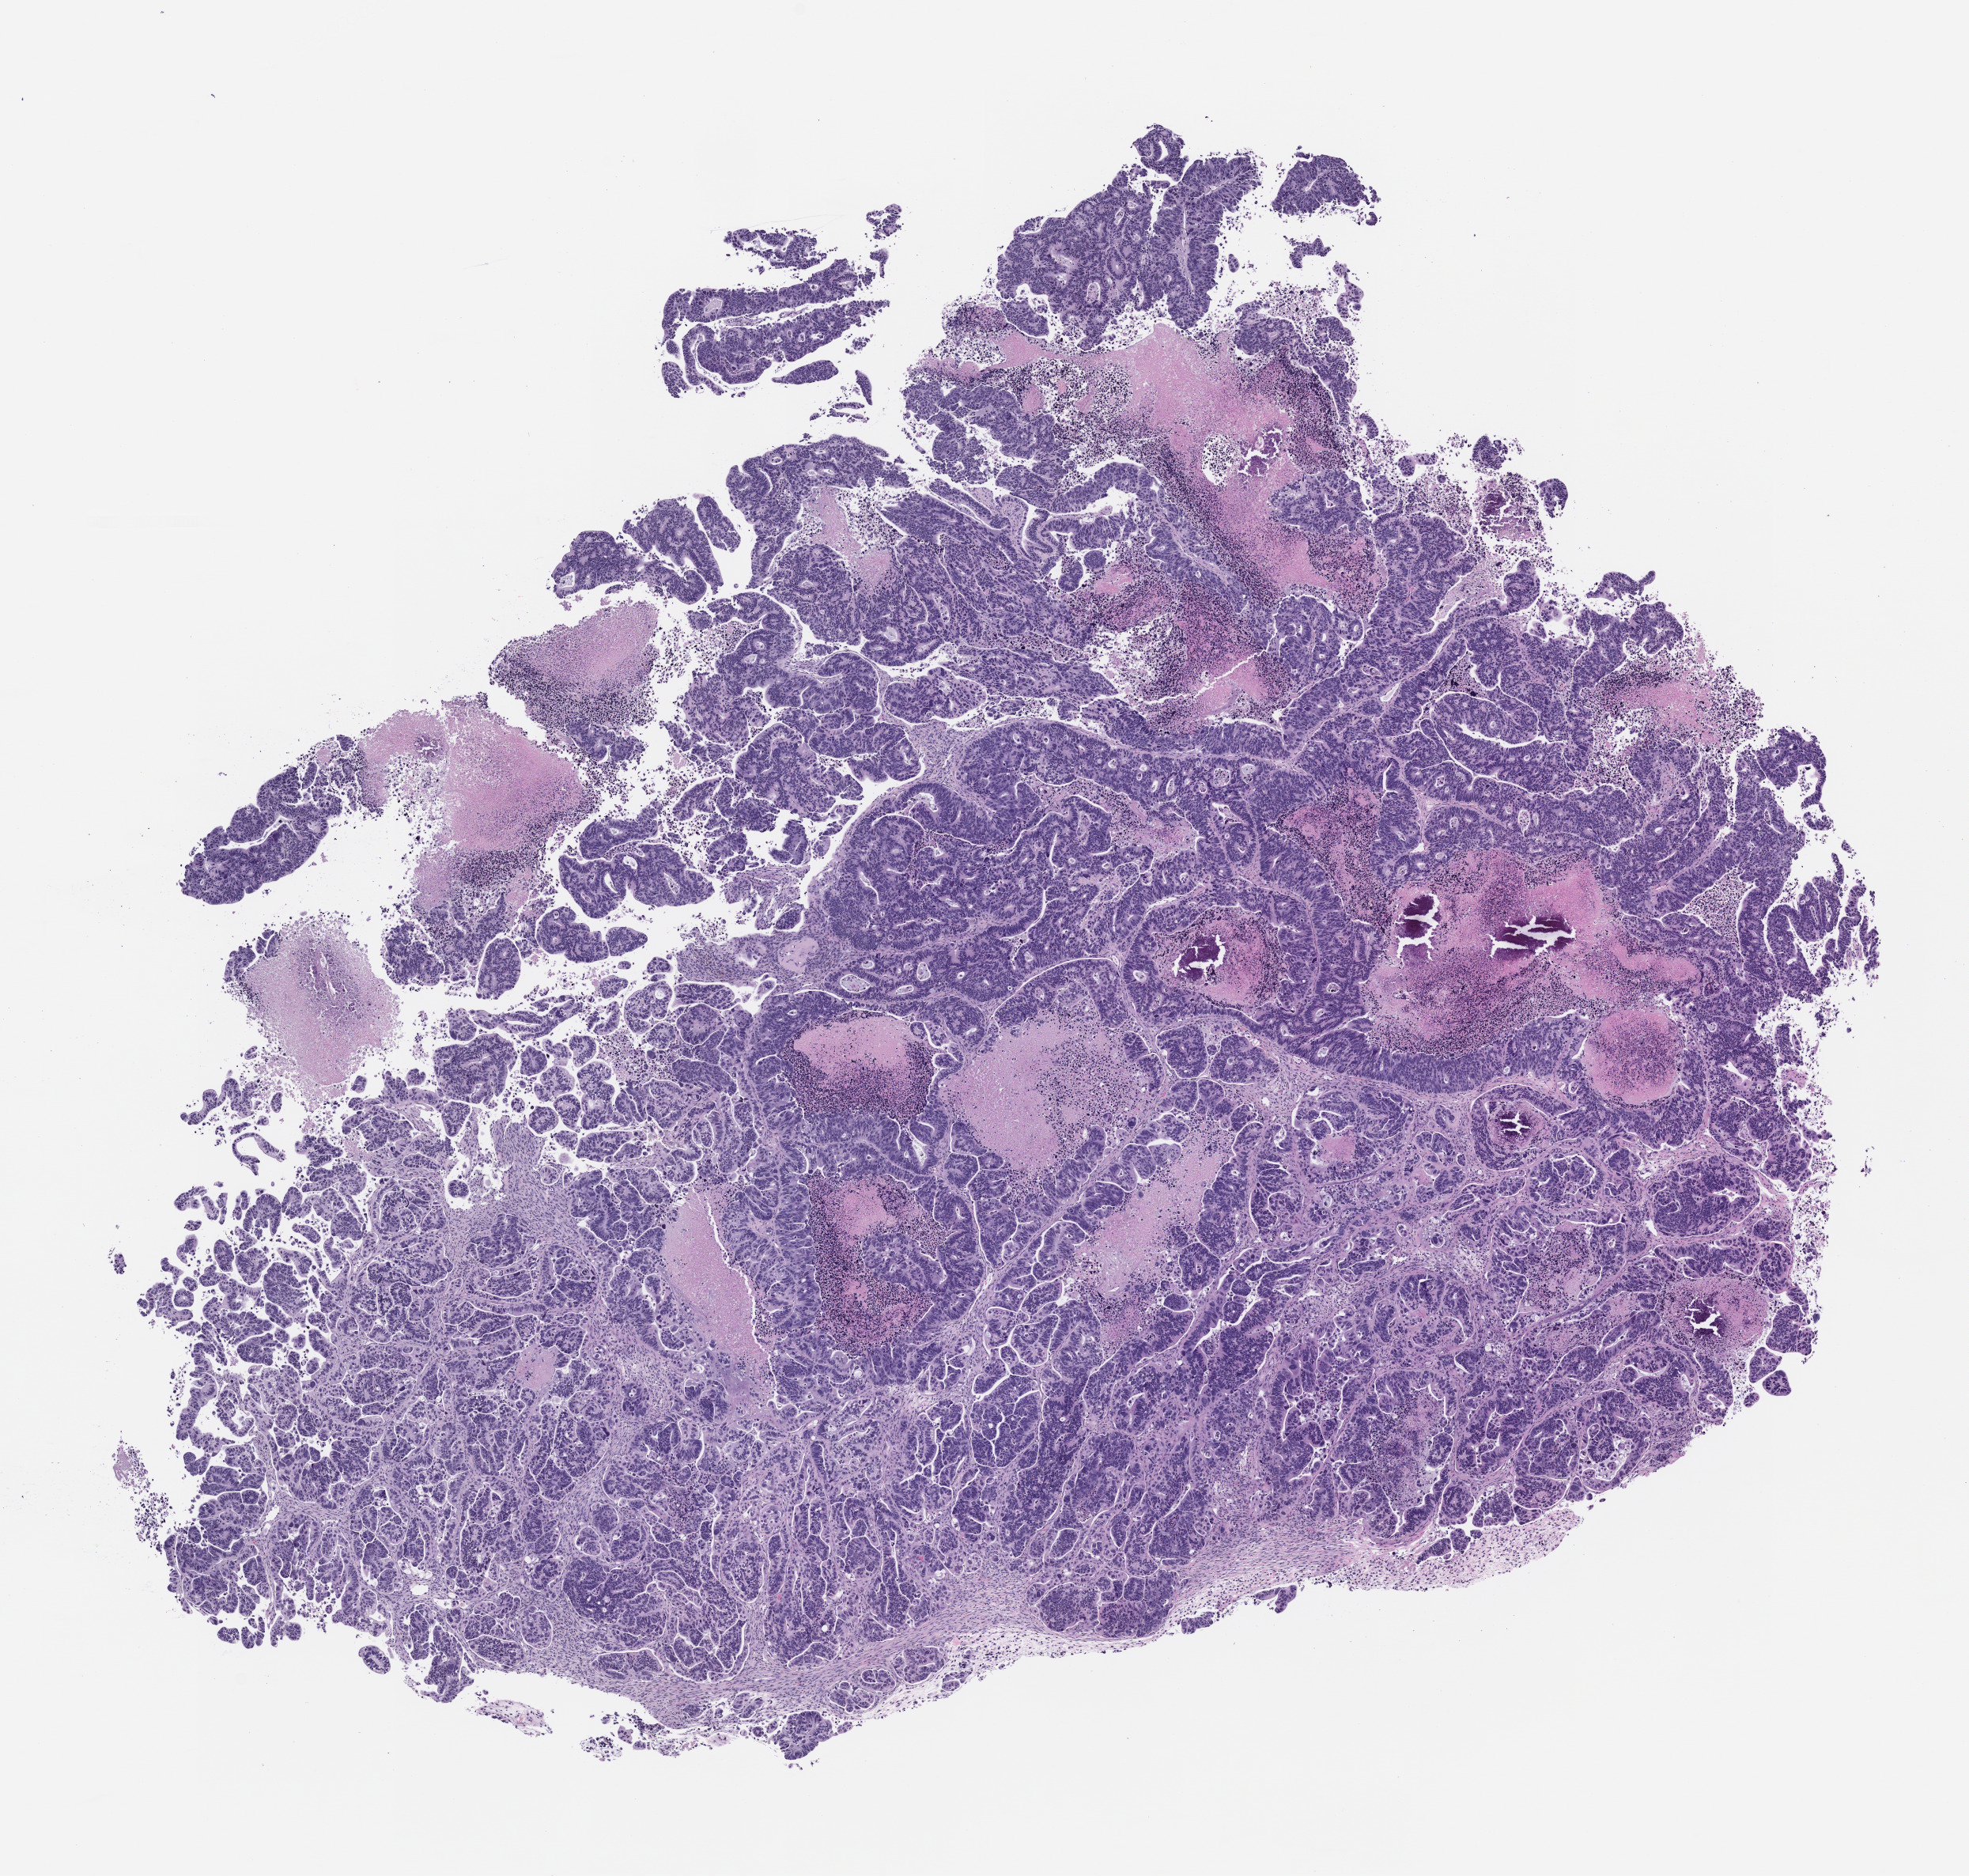
Whole-slide image, H&E: patient-derived xenograft (human tumor grown in a mouse), passage 1, a low-resolution overview of the entire scanned area, about 10.0 x 9.5 mm; FFPE section; originating tumor site category: colon.
Originating patient diagnosis: Colon Adenocarcinoma.